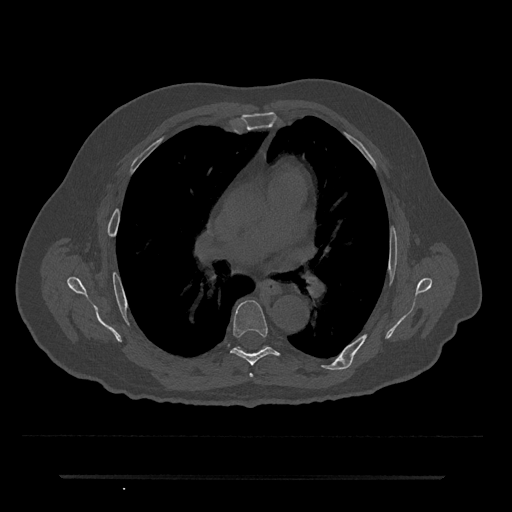
CT including the spine, one axial slice. Slice 431 of 797 in the series (ordered by position). Reconstruction kernel Br40s/3. Bone window (W 1800 / L 400 HU). 512 × 512 image matrix, field of view 437 × 437 mm. Male patient, age 69 years. From the clinical record (not read from this slice): primary cancer: prostate.
Annotated regions visible in this slice (semi-automatic segmentation, software-assisted and operator-edited):
- T5 vertebra: bounding box (x1, y1, x2, y2) in pixels: (249, 373, 253, 377)
- T6 vertebra: (230, 301, 279, 365)